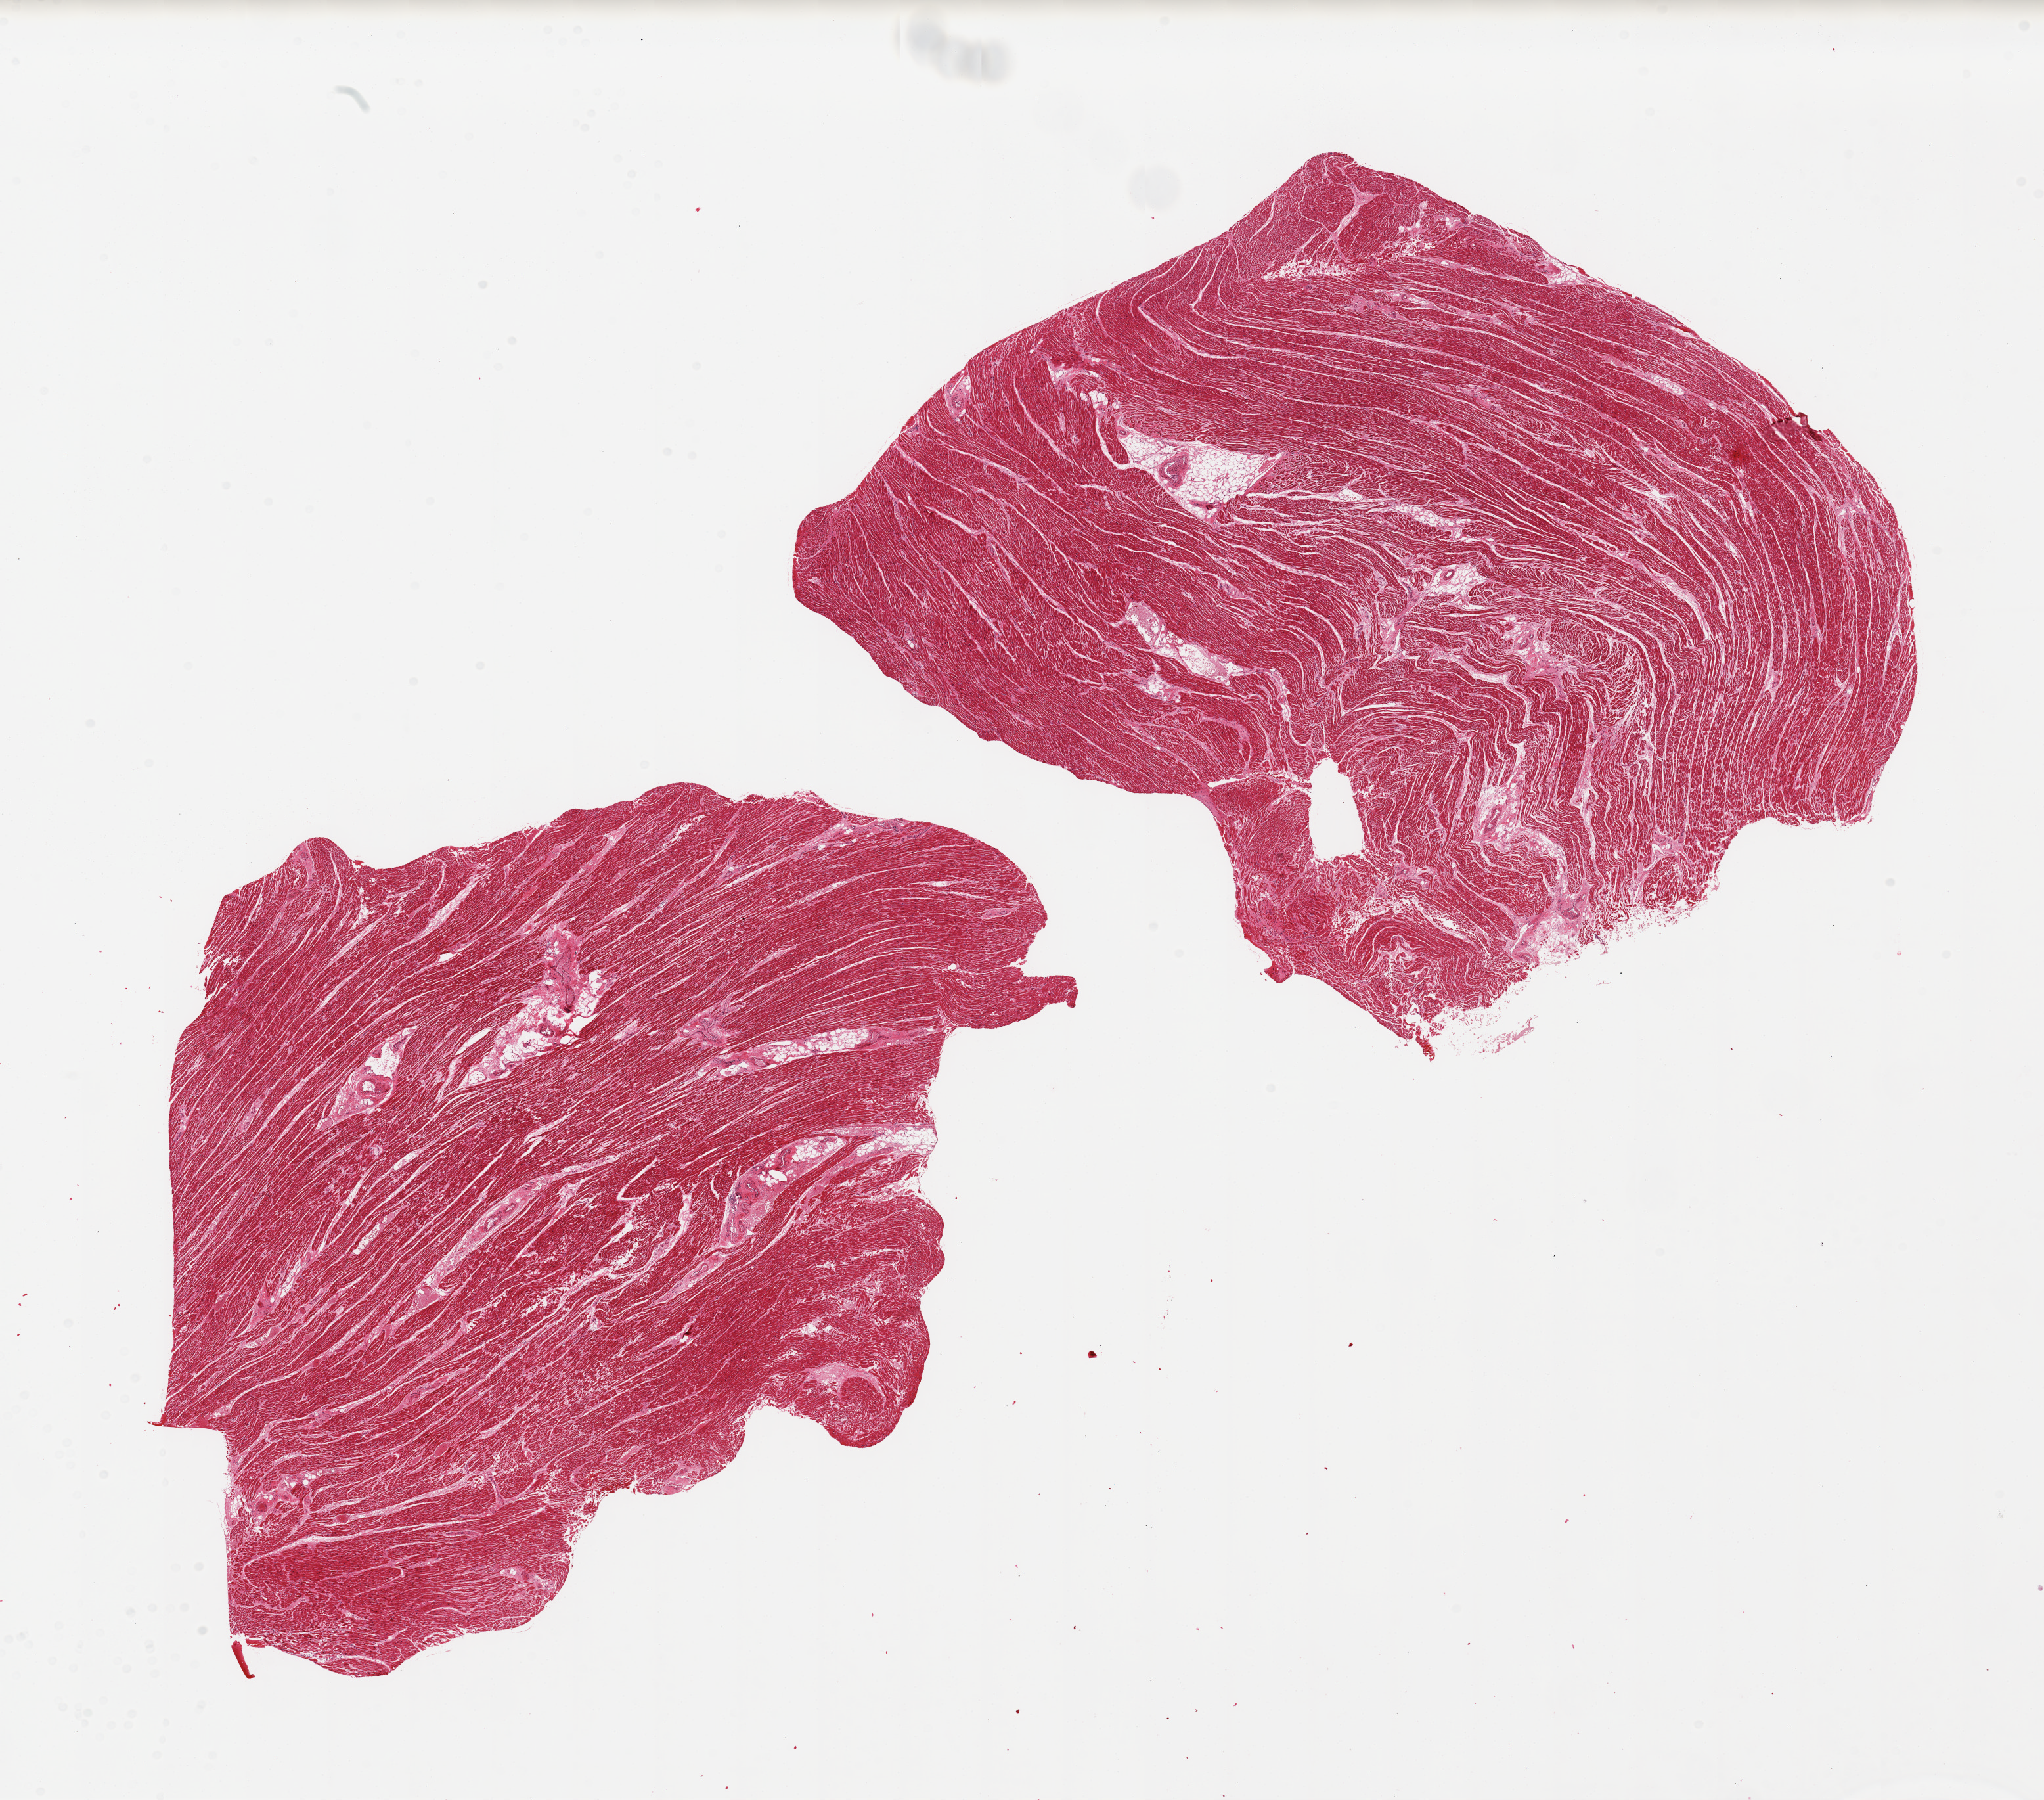
Haematoxylin and eosin whole-slide image, brightfield, shown as a low-resolution overview of the whole scanned area (about 24.6 x 21.7 mm), PAXgene-fixed, paraffin-embedded tissue, target tissue: heart, tissue donor sample. Male donor.
Reviewer comment on this tissue sample: 2 pieces; <5% internal fat.